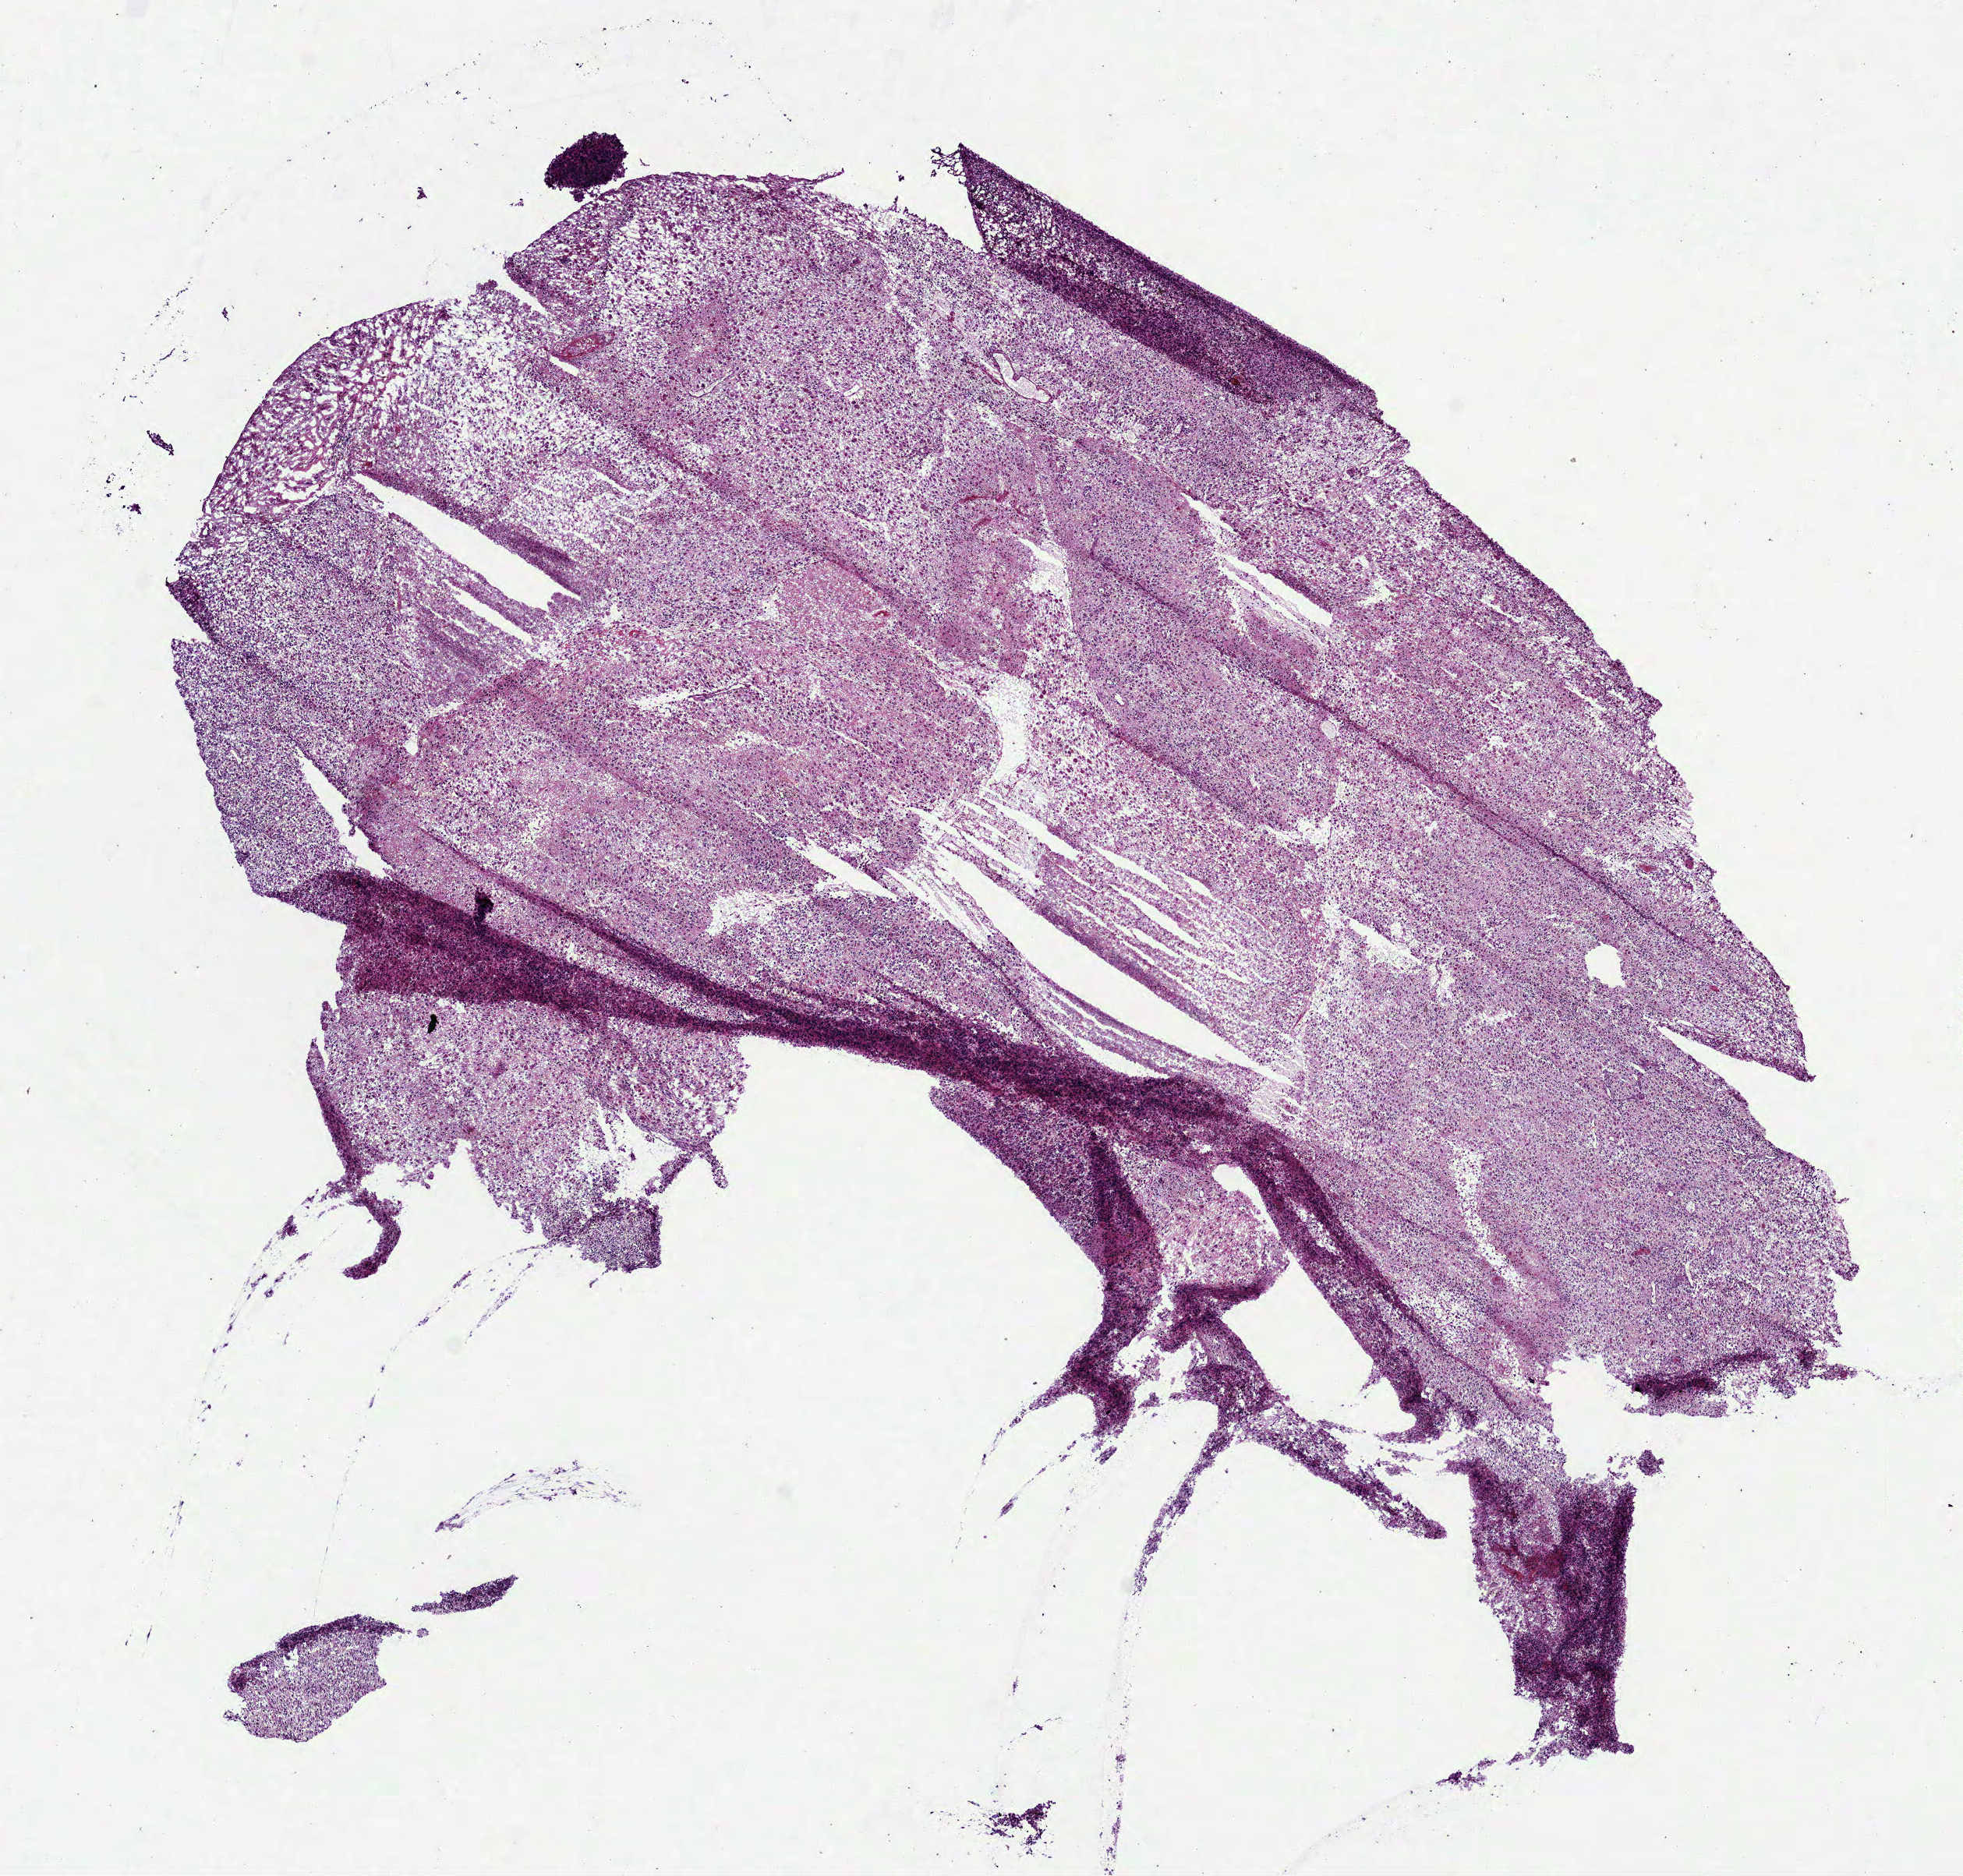
Digitized H&E-stained tissue section (whole slide) — a low-resolution overview of the entire scanned area, about 10.2 x 9.7 mm (slide scanned at 40x); frozen section; primary tumour sample from the brain. Male patient; age at initial diagnosis 33 years. Composition of this section per pathologist review: tumour cells 85%, tumour nuclei 85%, normal cells 0%, stromal cells 0%, necrosis 15%.
Pathologic diagnosis: Glioblastoma.